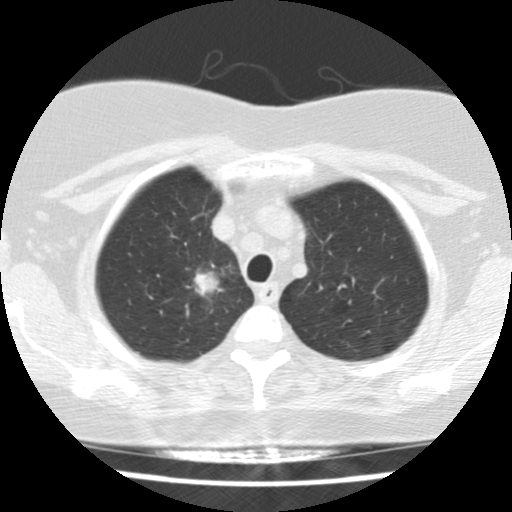
Axial slice from a low-dose chest CT screening exam; baseline annual screen; lung window (W 1500 / L -600 HU); standard (soft-tissue) reconstruction kernel (STANDARD). Female, age 58 years at enrolment.
Expert reader's lesion annotation, bounding box <169,241,247,321> (left, top, right, bottom; pixels). Screening reader's record for this exam (one nodule recorded; not confirmed to be the boxed lesion): non-calcified nodule or mass ≥4 mm, right upper lobe, 28 × 24 mm, spiculated (stellate) margins, soft tissue attenuation. Official screen result: positive, change unspecified: nodule(s) >= 4 mm or enlarging nodule(s), mass(es), or other non-specific abnormalities suspicious for lung cancer. Lung cancer was diagnosed 40 days after this screen: adenocarcinoma, NOS, right upper lobe, poorly differentiated (G3), stage IB (AJCC 6th edition), 29 mm at pathology.